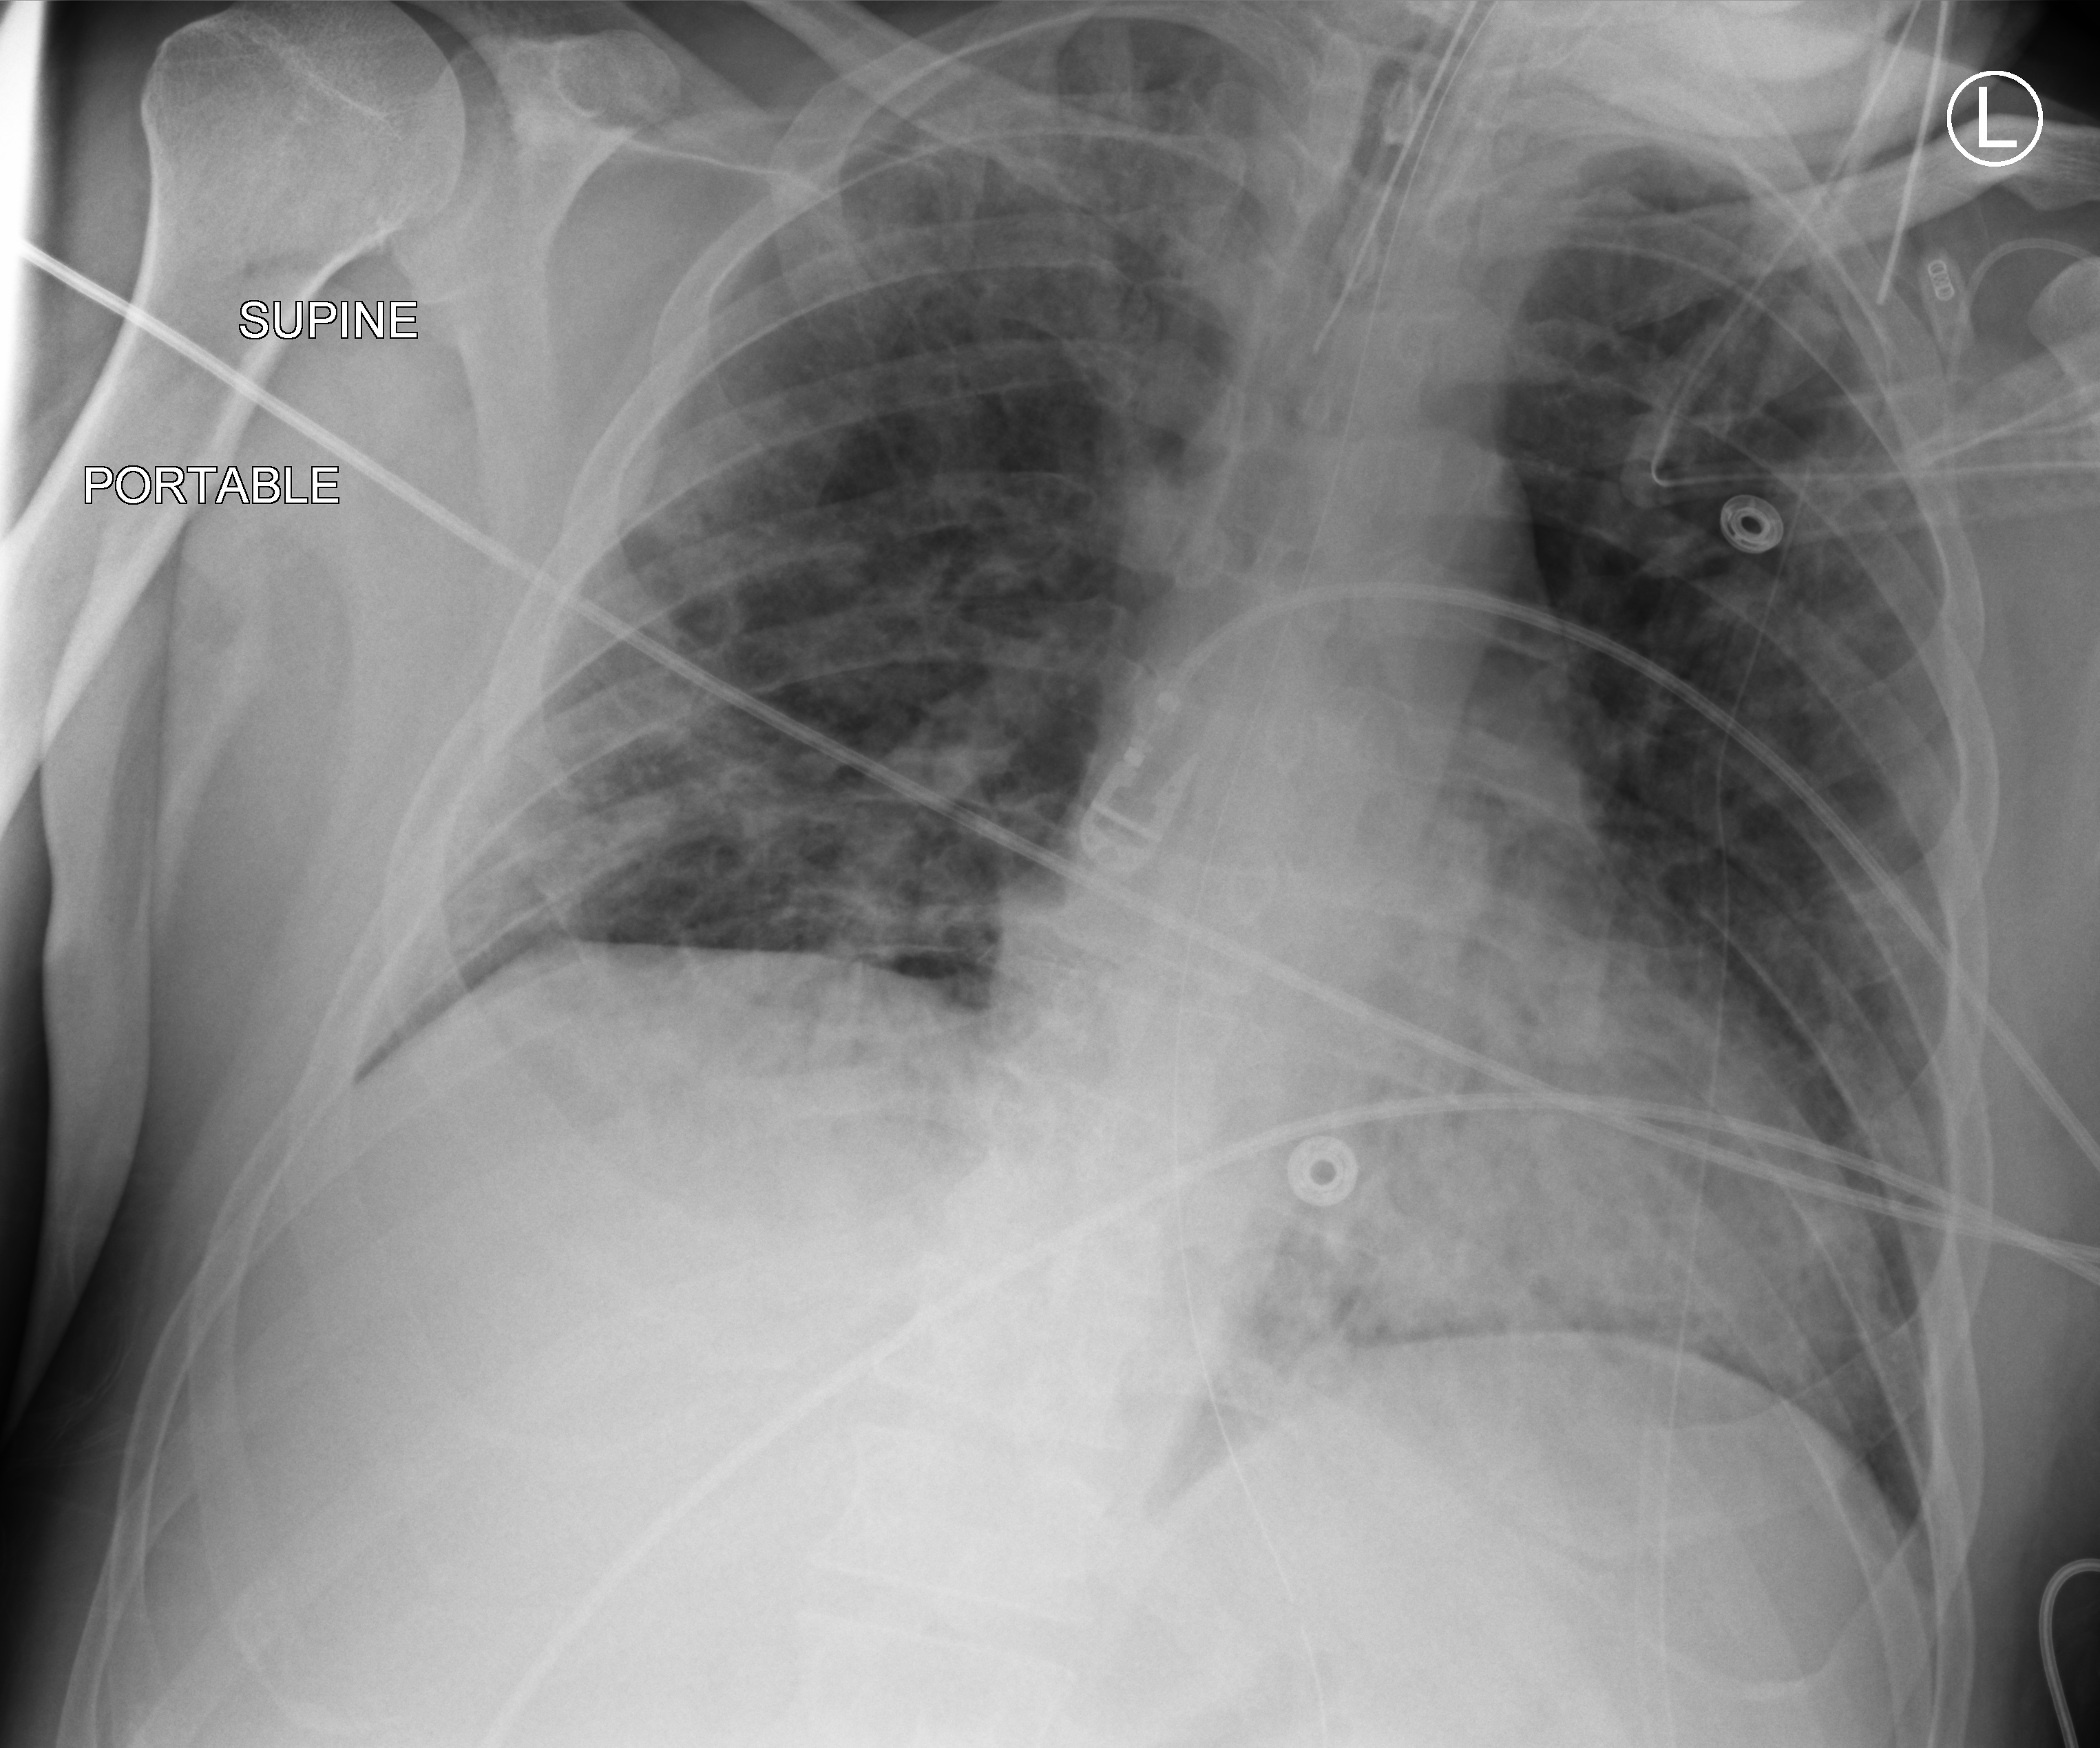
Chest X-ray (portable); anteroposterior (AP) projection. Patient hospitalised with COVID-19; male, aged 18–59 years.
Admission-level facts for this patient (not findings on this image; timing relative to this image not recorded): admitted to intensive care during this hospital stay: no; mechanically ventilated during this hospital stay: yes.